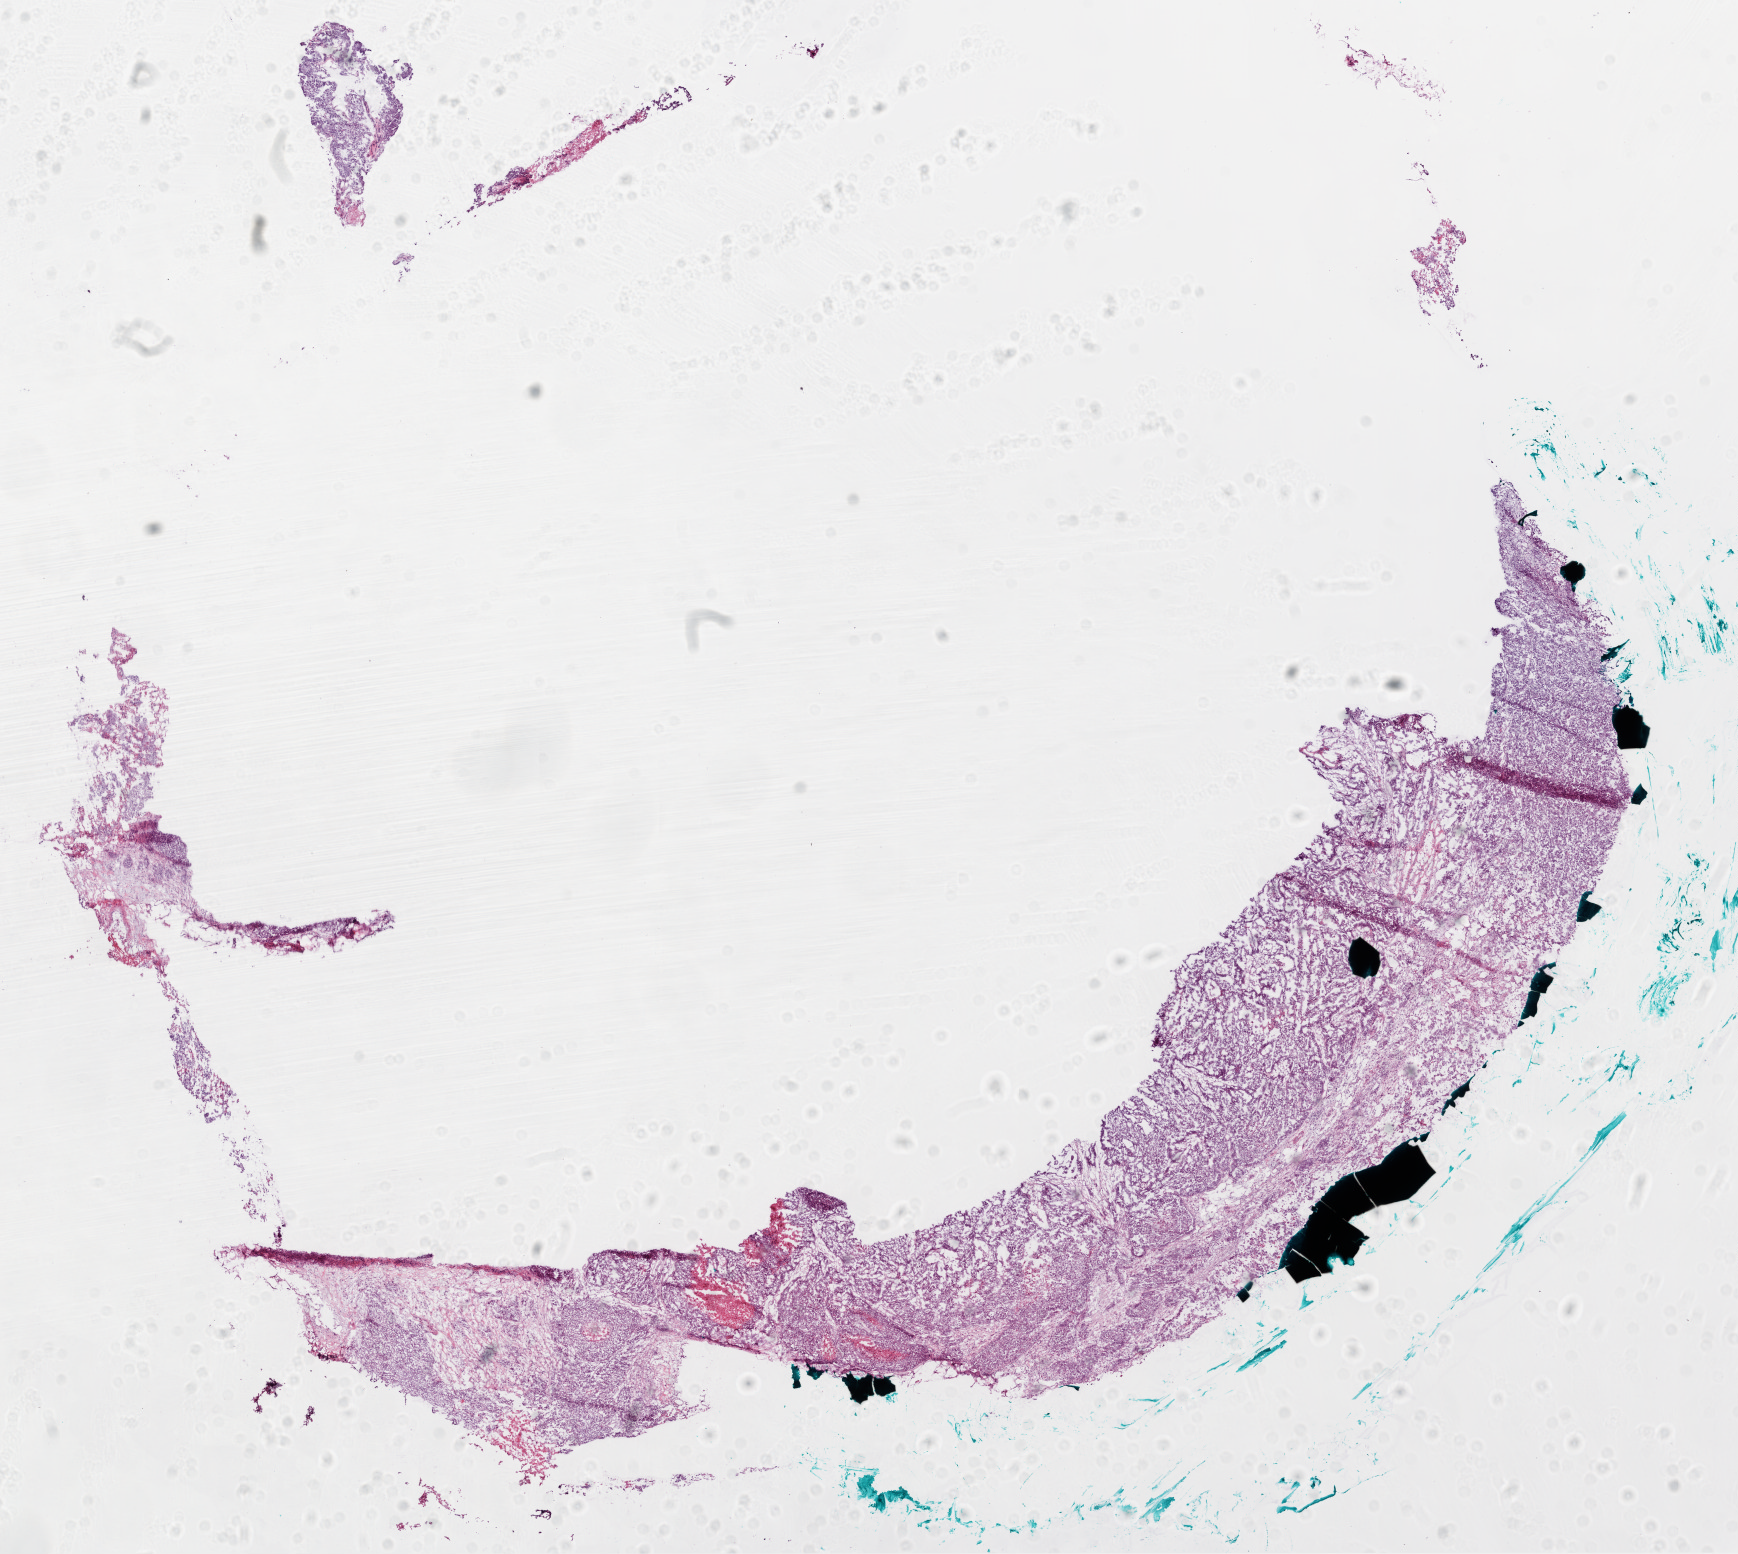
Whole-slide histology image, H&E-stained — shown as a low-resolution overview of the whole scanned area (about 14.0 x 12.5 mm), frozen section from the bottom of the tissue portion, sample: primary tumour, ovary. Female patient; age at initial diagnosis 60 years. Histologic grade: G3 (poorly differentiated). Slide review estimates, as recorded: tumour cells 75%, tumour nuclei 80%, normal cells 20%, necrosis 5%.
Pathologic diagnosis: Serous cystadenocarcinoma, NOS. Laterality: bilateral. FIGO stage: IV.